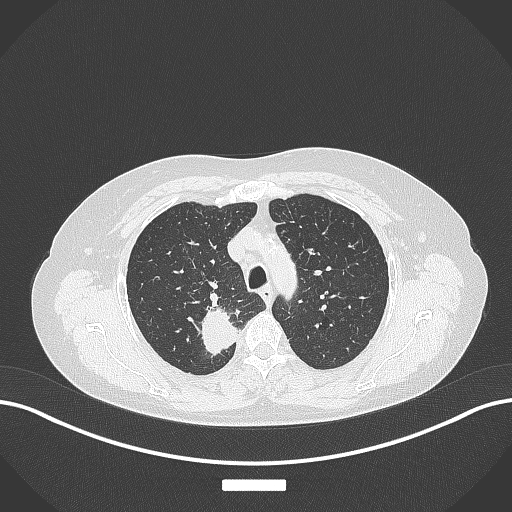
Chest CT, one axial slice. Slice 296 of 357 in the series (ordered by position). 120 kVp. Lung window (W 1500 / L -600 HU). 1 mm slice thickness. 512 × 512 image matrix. Patient: female, 62 years. Case-level facts recorded for this patient, not image findings: clinical TNM (as recorded): T1c N1 M0.
Outlined on this slice (bounding box drawn by a radiologist):
- lung tumour (recorded histology: squamous cell carcinoma): bounding box <189,297,233,359> (left, top, right, bottom; pixels)